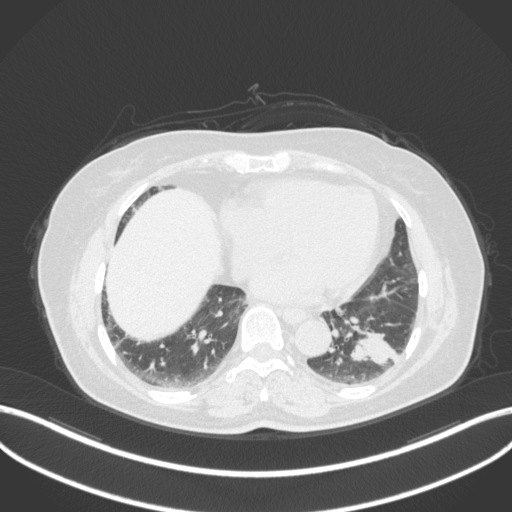
Chest CT, one axial slice; slice 131 of 307 in the series (ordered by position); lung window (W 1500 / L -600 HU); 512 × 512 image matrix, field of view 400 × 400 mm. Female patient, age 59 years. From the clinical record (not read from this slice): clinical TNM (as recorded): T2a N0 M0; histopathological grade: G2-3.
Outlined on this slice (bounding box drawn by a radiologist):
- lung tumour (recorded histology: adenocarcinoma): bounding box [x1, y1, x2, y2] px = [345, 325, 403, 372]